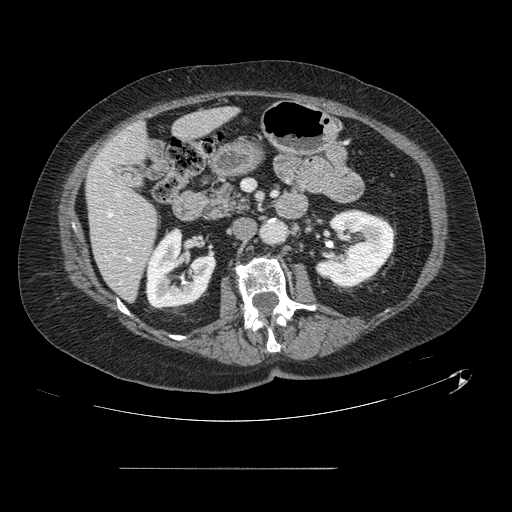
Contrast-enhanced abdominal CT, one axial slice; slice 45 of 148 in the series (ordered by position); intravenous contrast given; soft-tissue window (W 400 / L 40 HU); 512 × 512 image matrix, field of view 439 × 439 mm. Female patient, age 75 years. From the clinical record (not read from this slice): diagnosis: colorectal cancer liver metastases, imaged before liver resection; multiple liver metastases: no; largest metastasis: 2.4 cm.
Annotated regions visible in this slice (outlined manually by an expert reader):
- hepatic veins: bounding box [x1, y1, x2, y2] px = [109, 213, 131, 261]
- liver: [87, 109, 234, 300]
- planned liver remnant (the part of the liver to remain after resection): [87, 109, 233, 300]